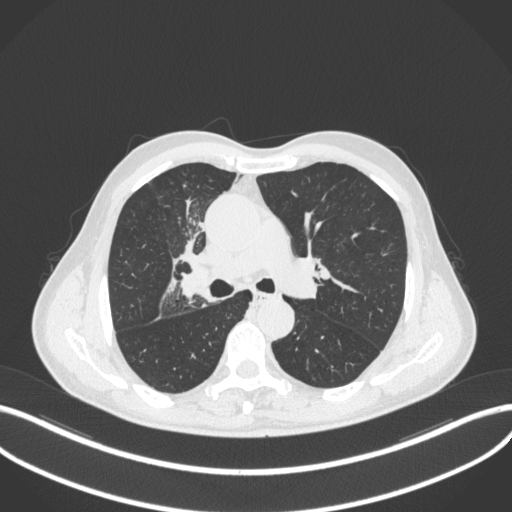
Chest CT, one axial slice. Position 303 of 490 along the scan axis. 120 kVp. Lung window (W 1500 / L -600 HU). 512 × 512 image matrix, field of view 400 × 400 mm. Male patient, age 69 years. From the clinical record (not read from this slice): clinical TNM (as recorded): T2a N0 M0.
Annotated regions visible in this slice (rectangle marked by the reading radiologist):
- lung tumour (recorded histology: adenocarcinoma): bounding box <176,262,209,303> (left, top, right, bottom; pixels)